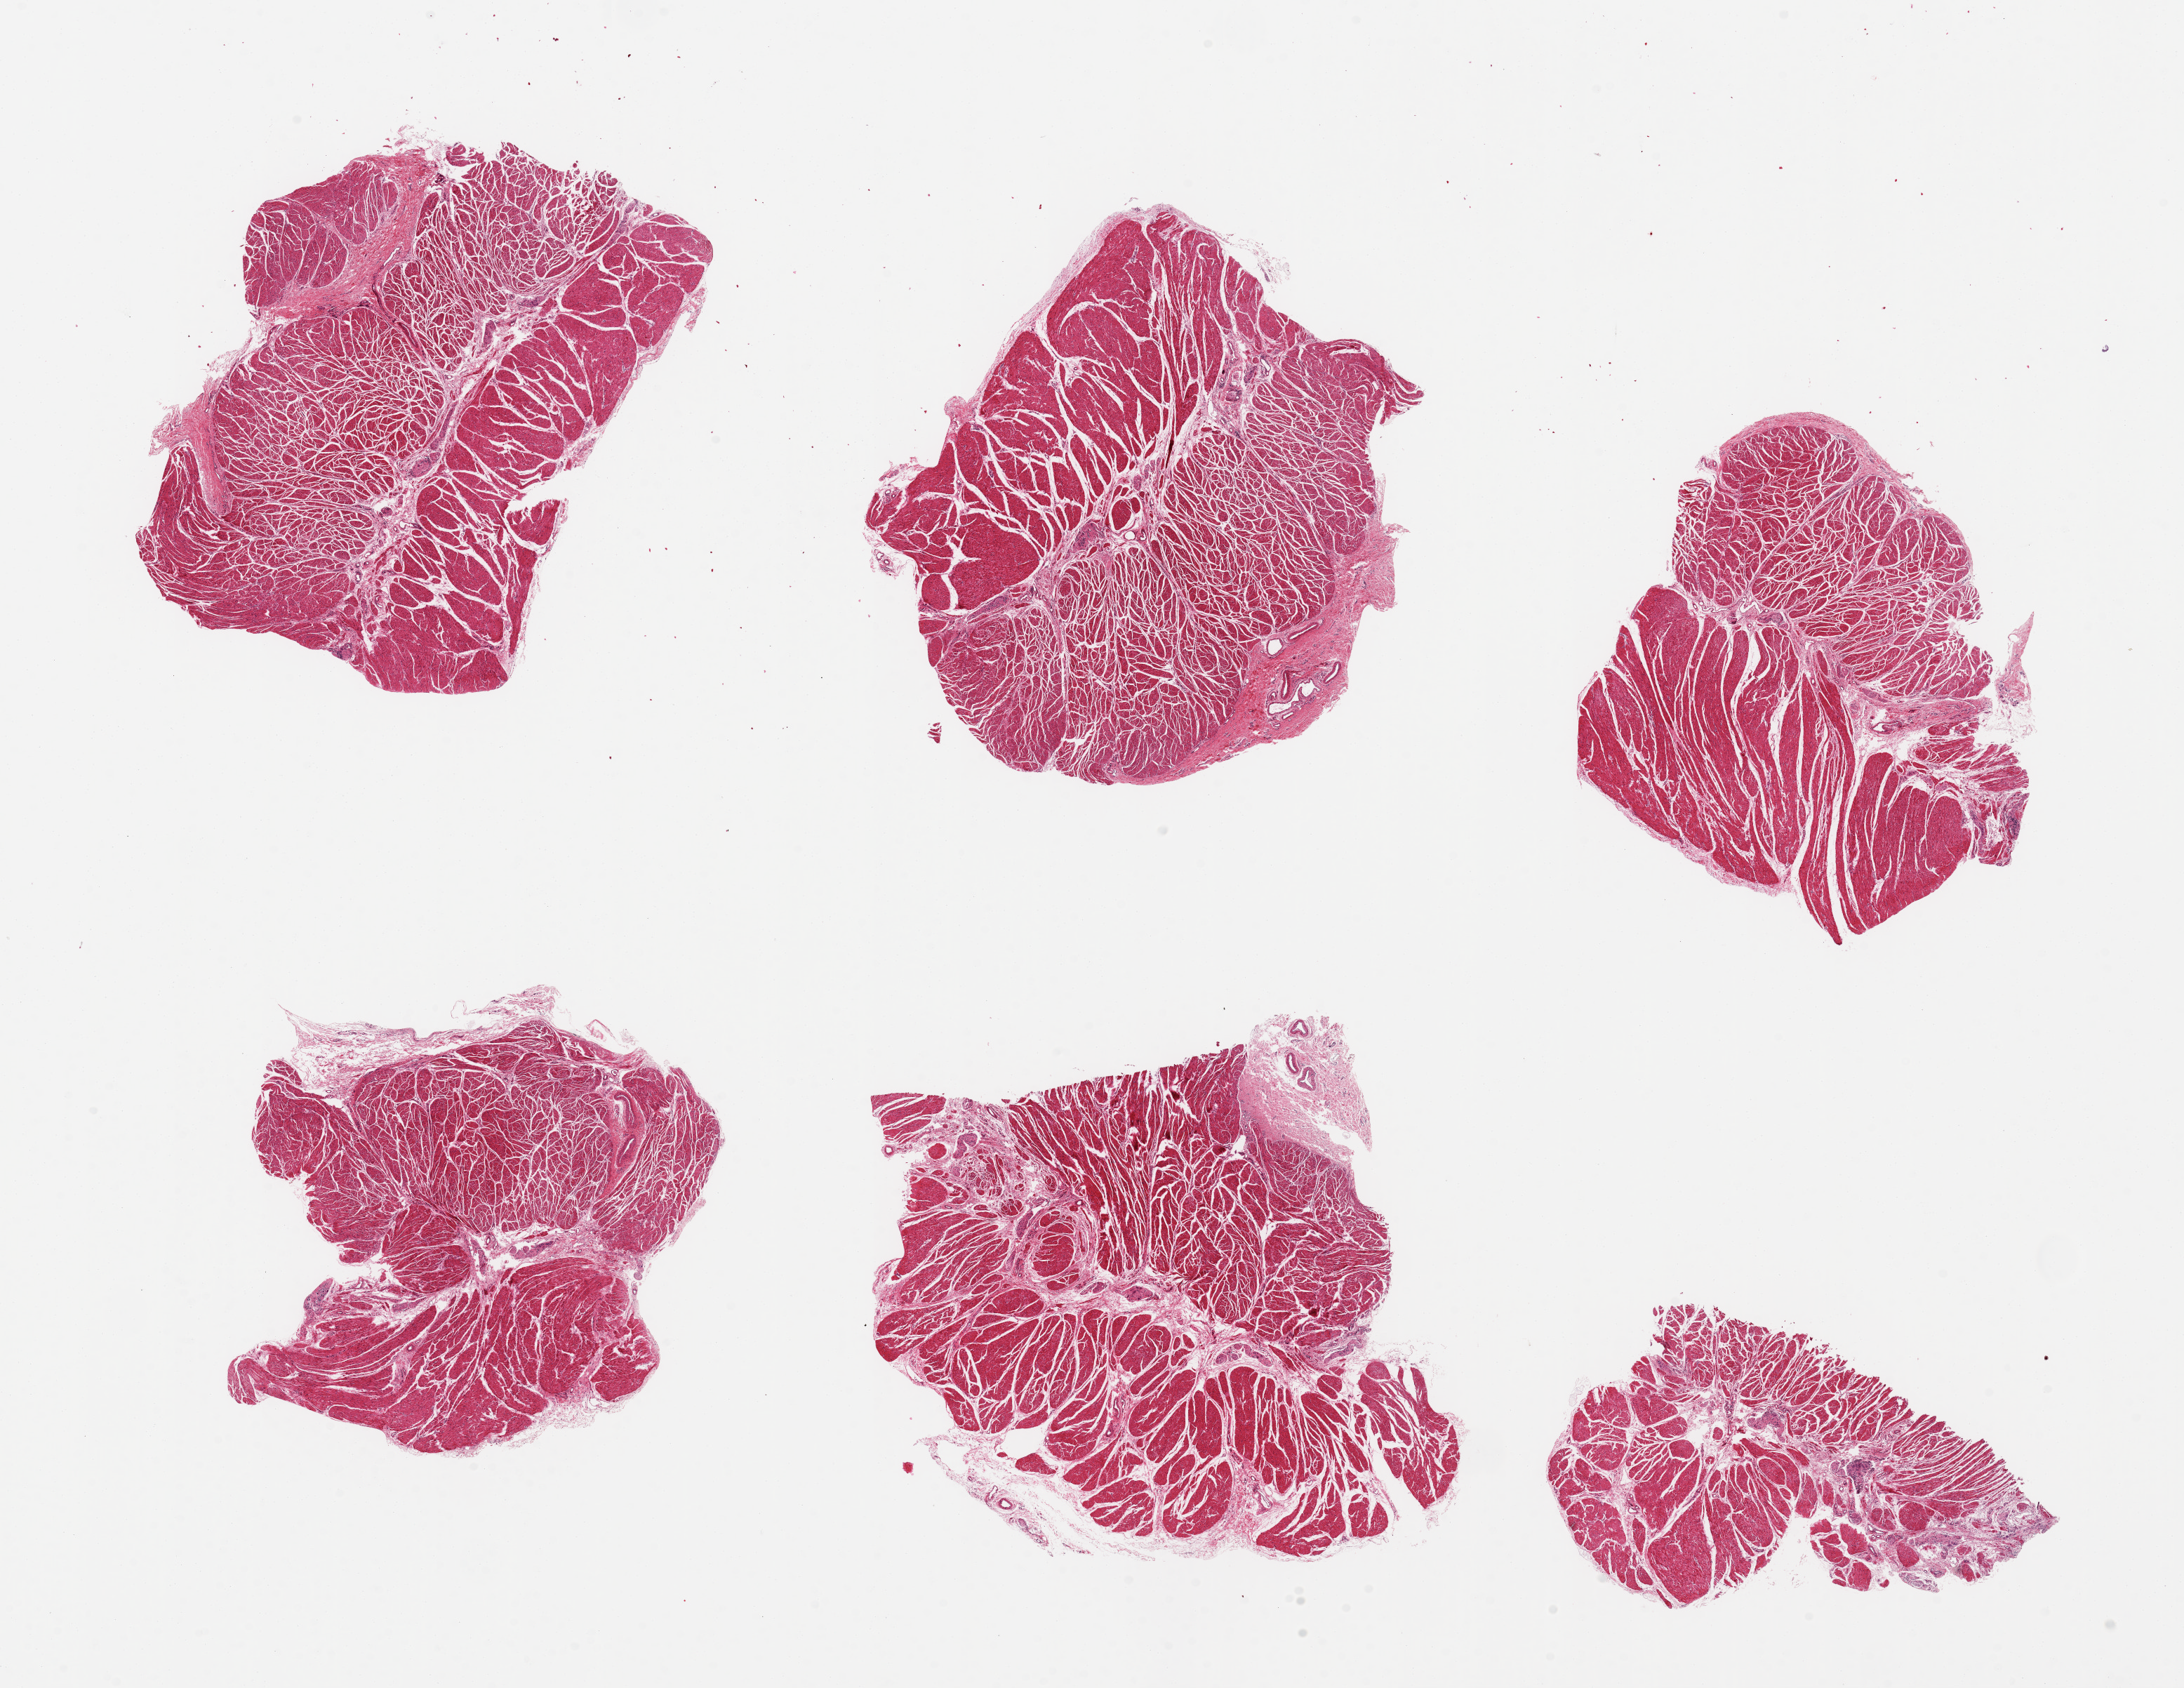
H&E whole-slide image, whole scanned area (about 24.6 x 19.0 mm, from a 20x scan) shown as a low-resolution overview; PAXgene-fixed paraffin-embedded (PFPE) section; target tissue: esophageal muscle; donor tissue sample. Donor sex: female.
* review note (as recorded): 6 pieces, ~5x5mm